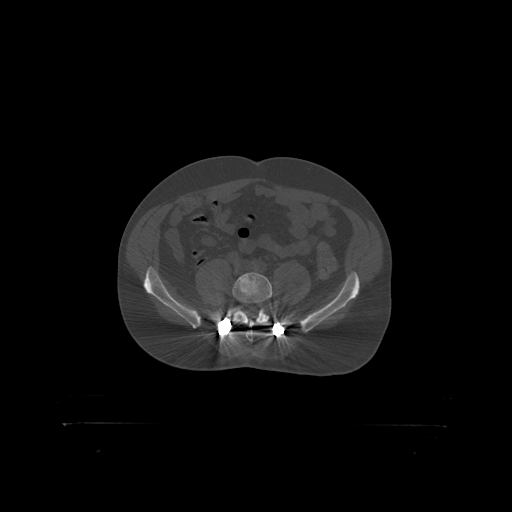
CT including the spine, one axial slice. Slice 201 of 399 in the series (ordered by position). Reconstruction kernel STANDARD. 120 kVp. Bone window (W 1800 / L 400 HU). 512 × 512 image matrix. Patient: male, 46 years. From the clinical record (not read from this slice): primary cancer: skin.
Annotated regions visible in this slice (semi-automatically segmented with operator editing):
- L5 vertebra: bounding box [x1, y1, x2, y2] px = [232, 273, 273, 319]